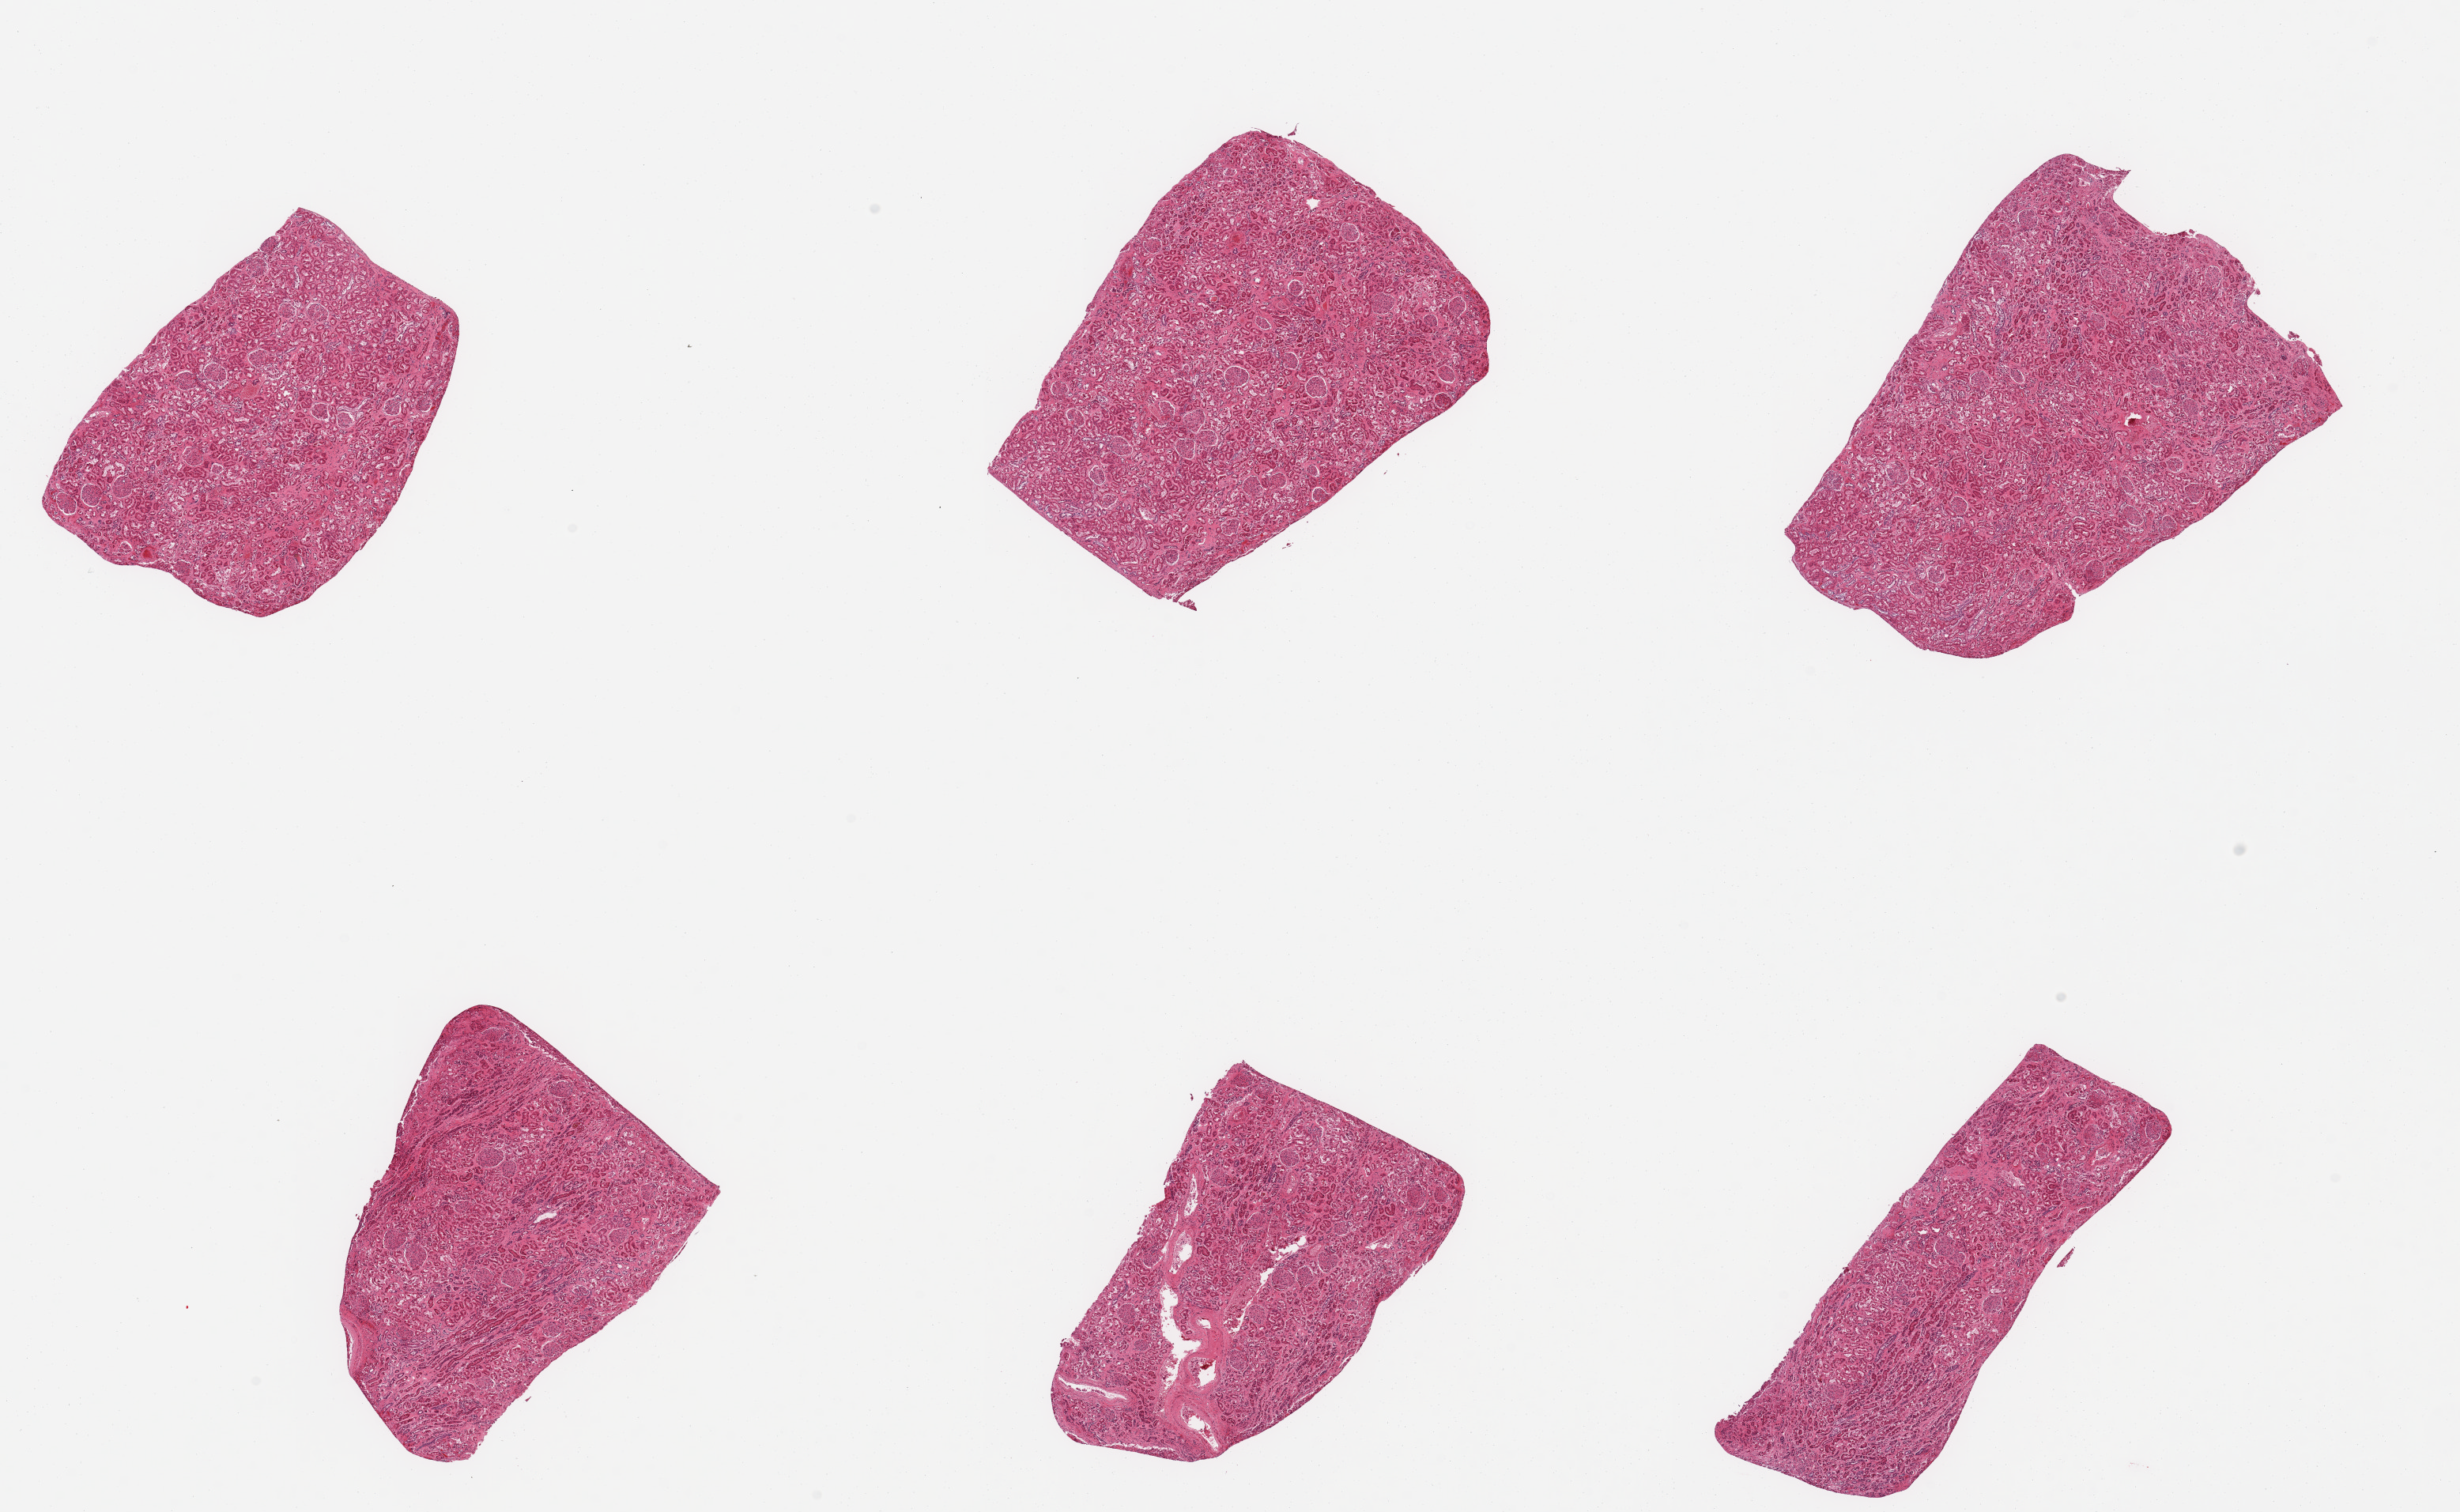
Digitized hematoxylin and eosin (H&E)-stained section, a low-resolution overview of the entire scanned area, about 24.6 x 15.1 mm (slide scanned at 20x). PAXgene-fixed, paraffin-embedded tissue. Target tissue: renal cortex. Donor tissue sample.
Review note (as recorded): 6 pieces; tubules poorly preserved; glomeruli OK; mild interstitial fibrosis.